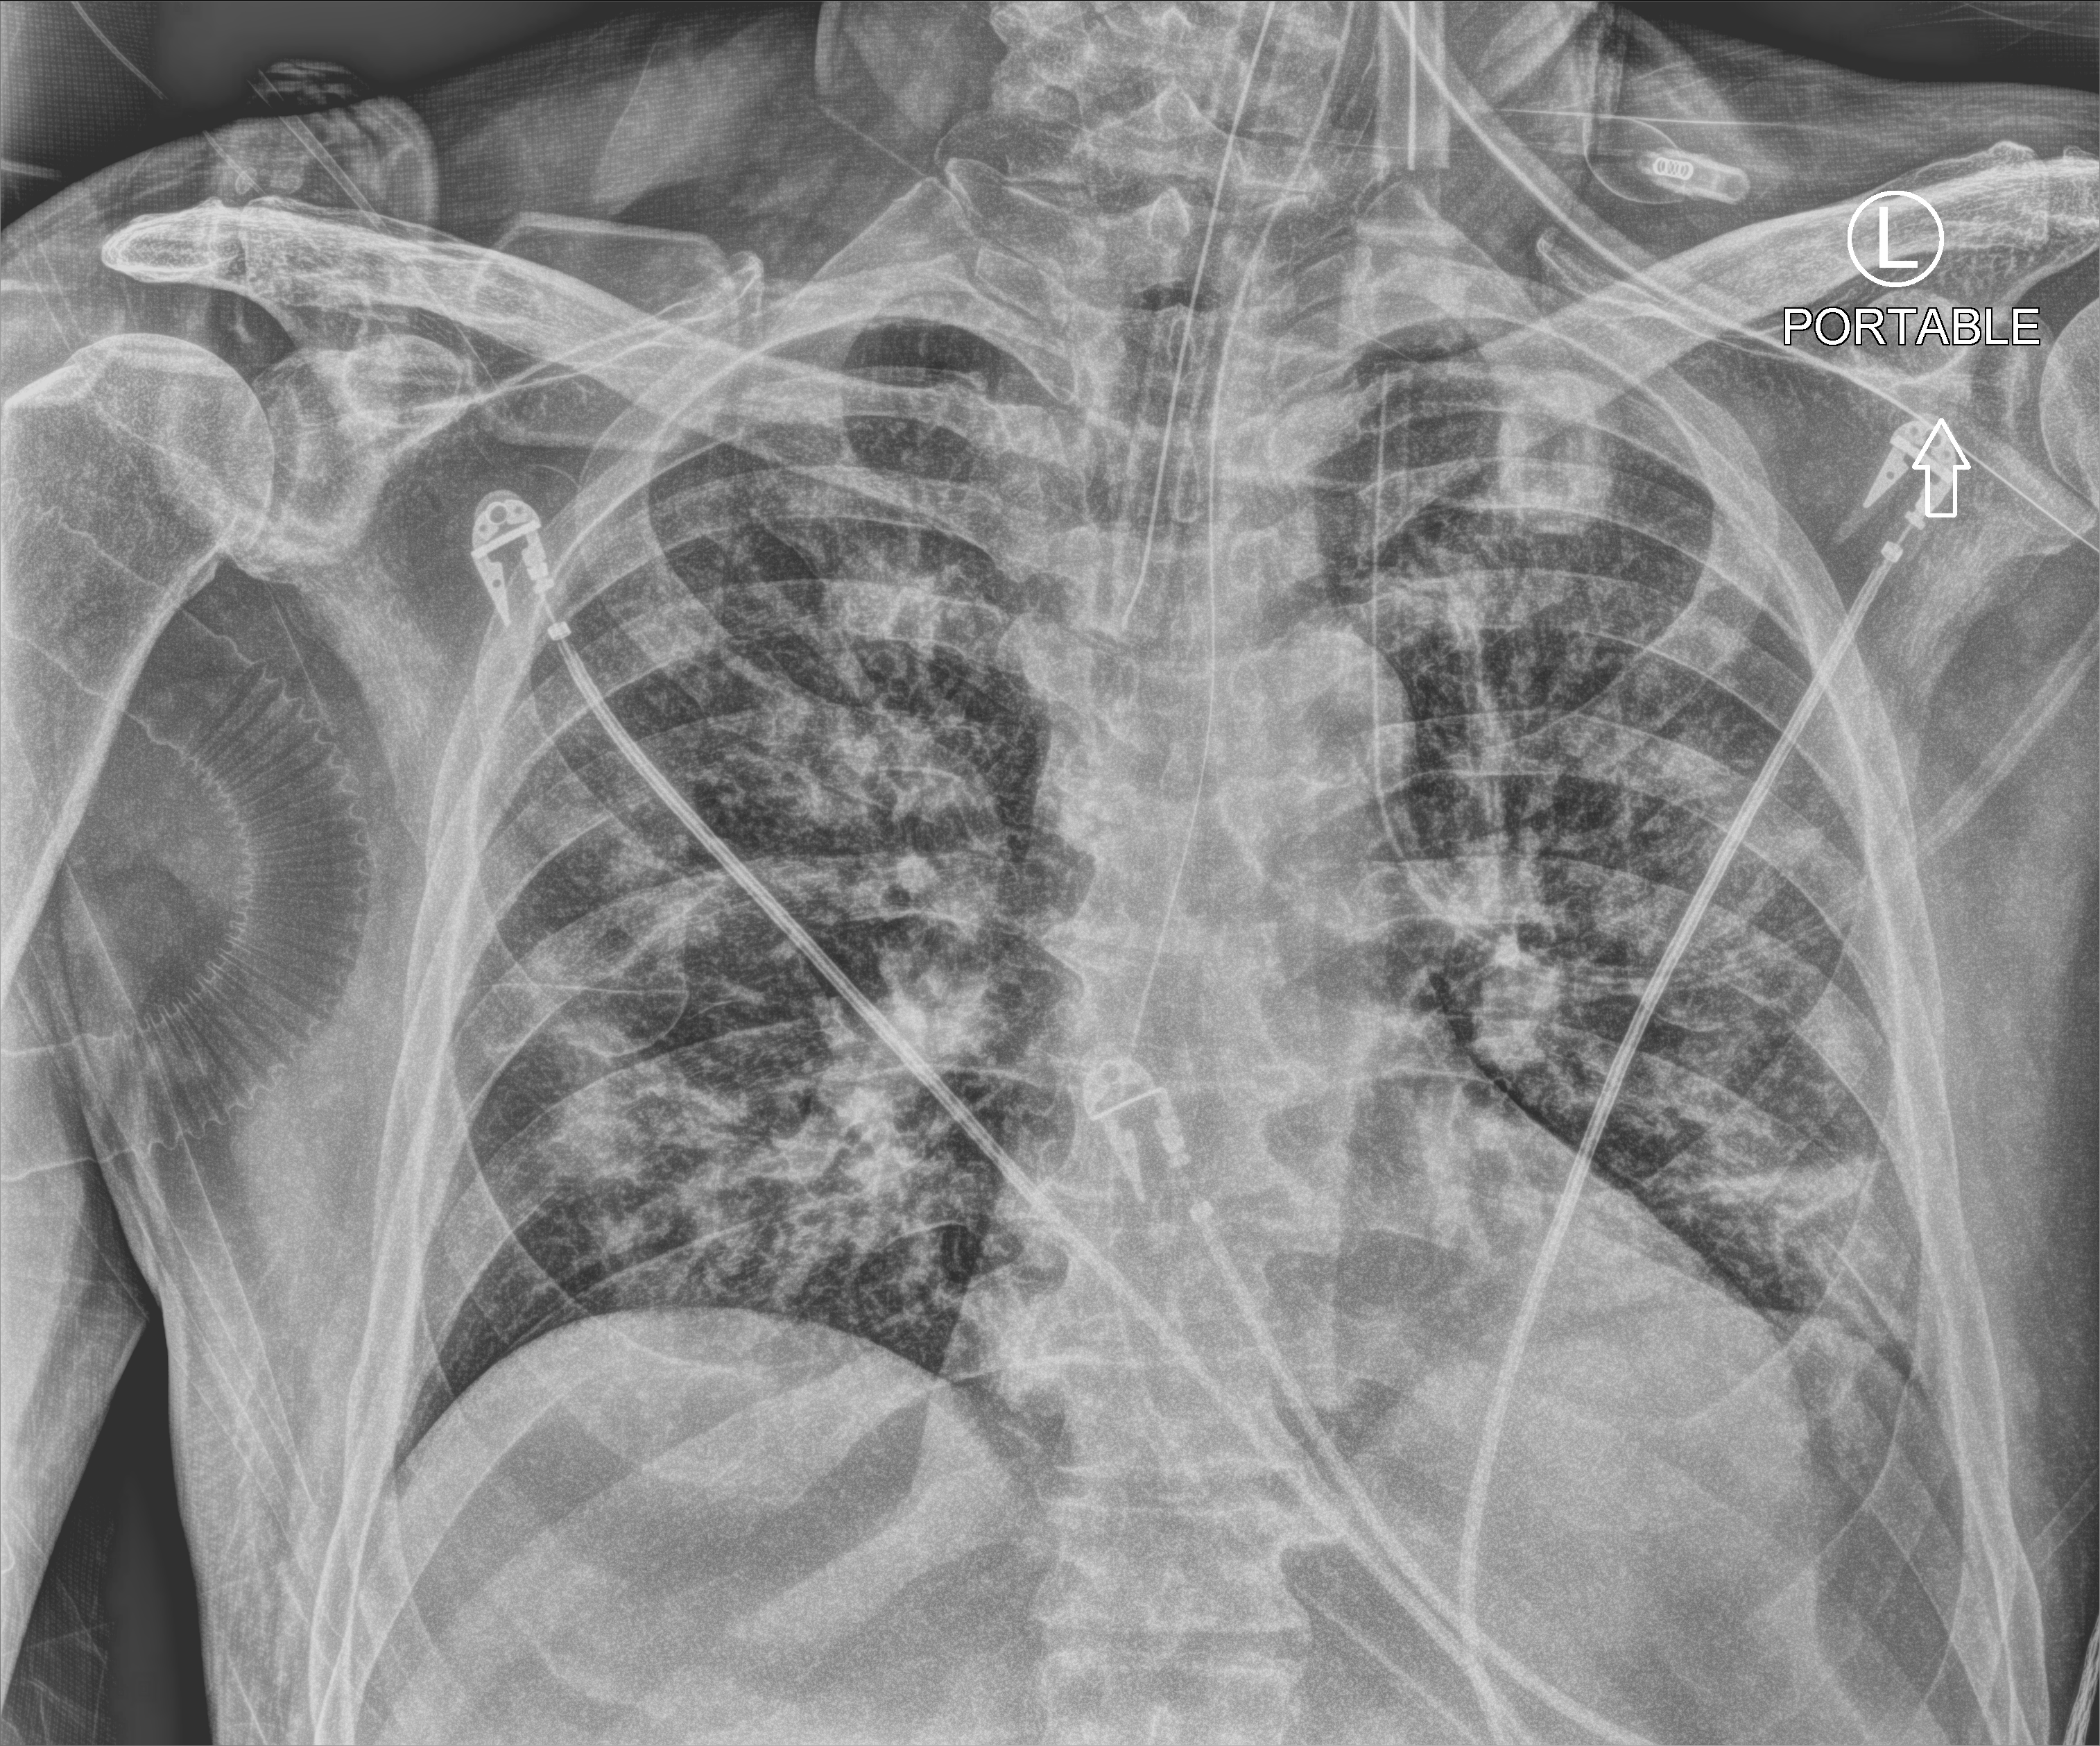
Bedside chest radiograph (computed radiography), anteroposterior (AP) projection. Male patient hospitalised with COVID-19, age 60–74 years.
Hospital-stay facts (about this admission, not read from this image; timing relative to this image not recorded): hypertension (admission record): yes; mechanically ventilated during this hospital stay: yes; other chronic lung disease (admission record): no.